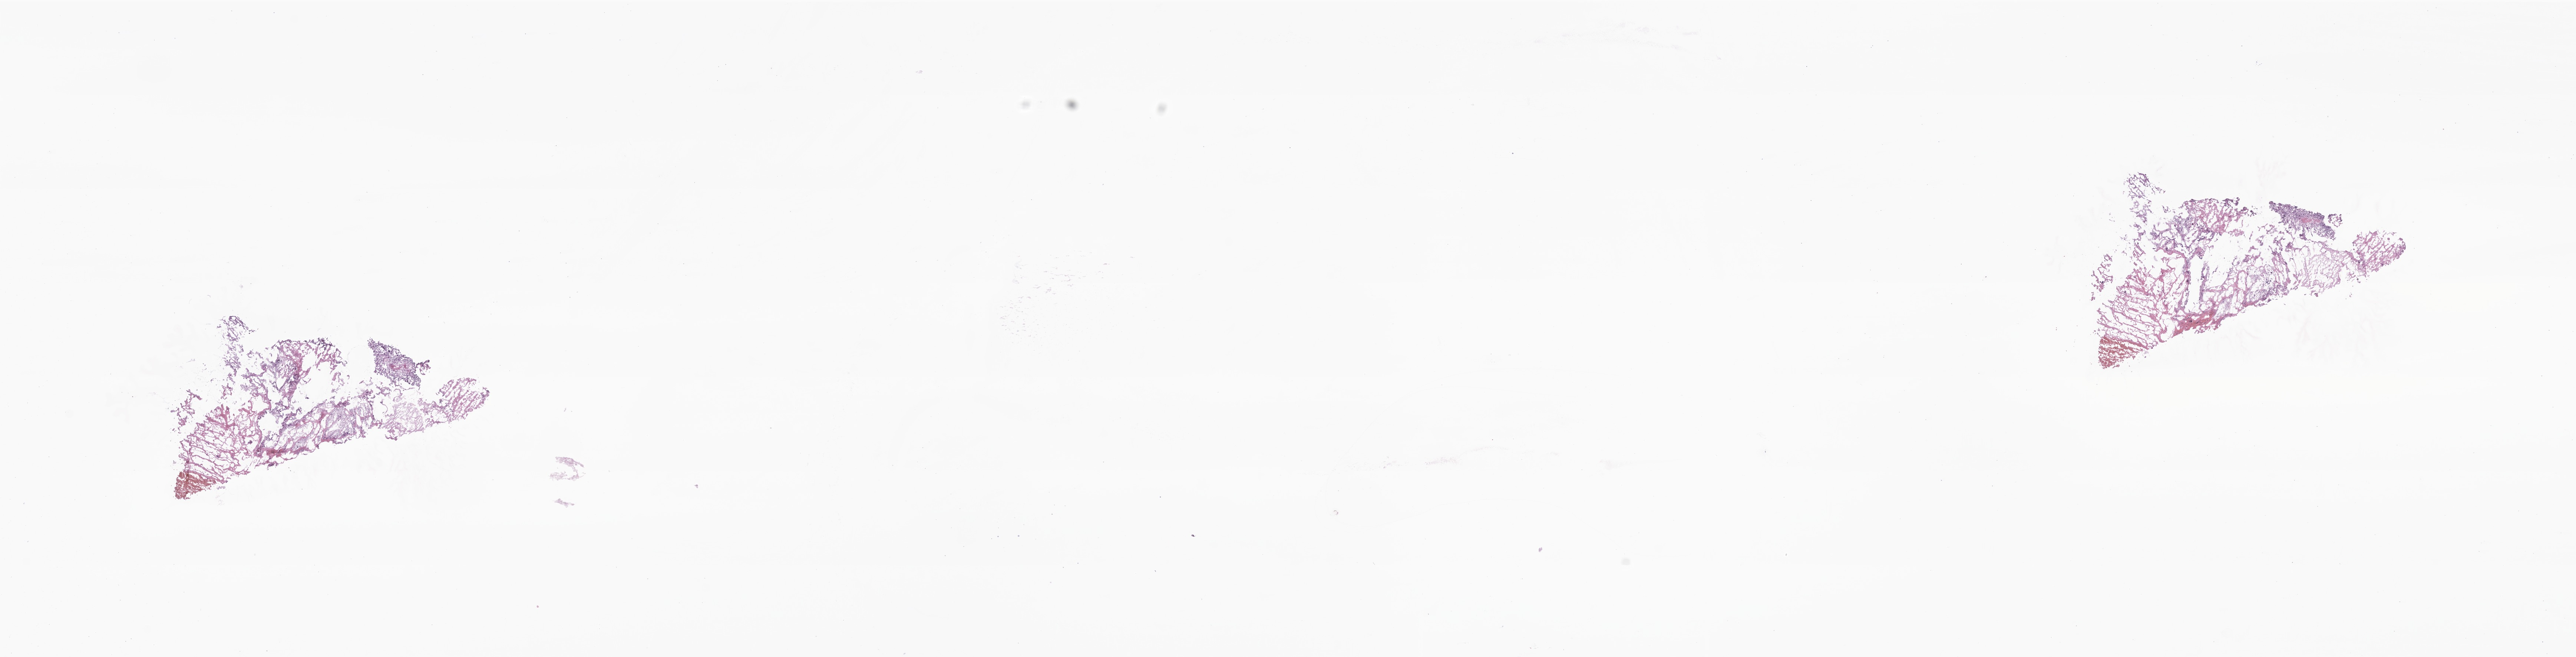
Haematoxylin and eosin whole-slide image of tumor tissue from the brain, low-resolution overview of the scanned area, about 29.3 x 7.5 mm. Frozen section. Patient female; age 106 months (8 years 10 months).
- diagnosis: Neoplasm, uncertain whether benign or malignant